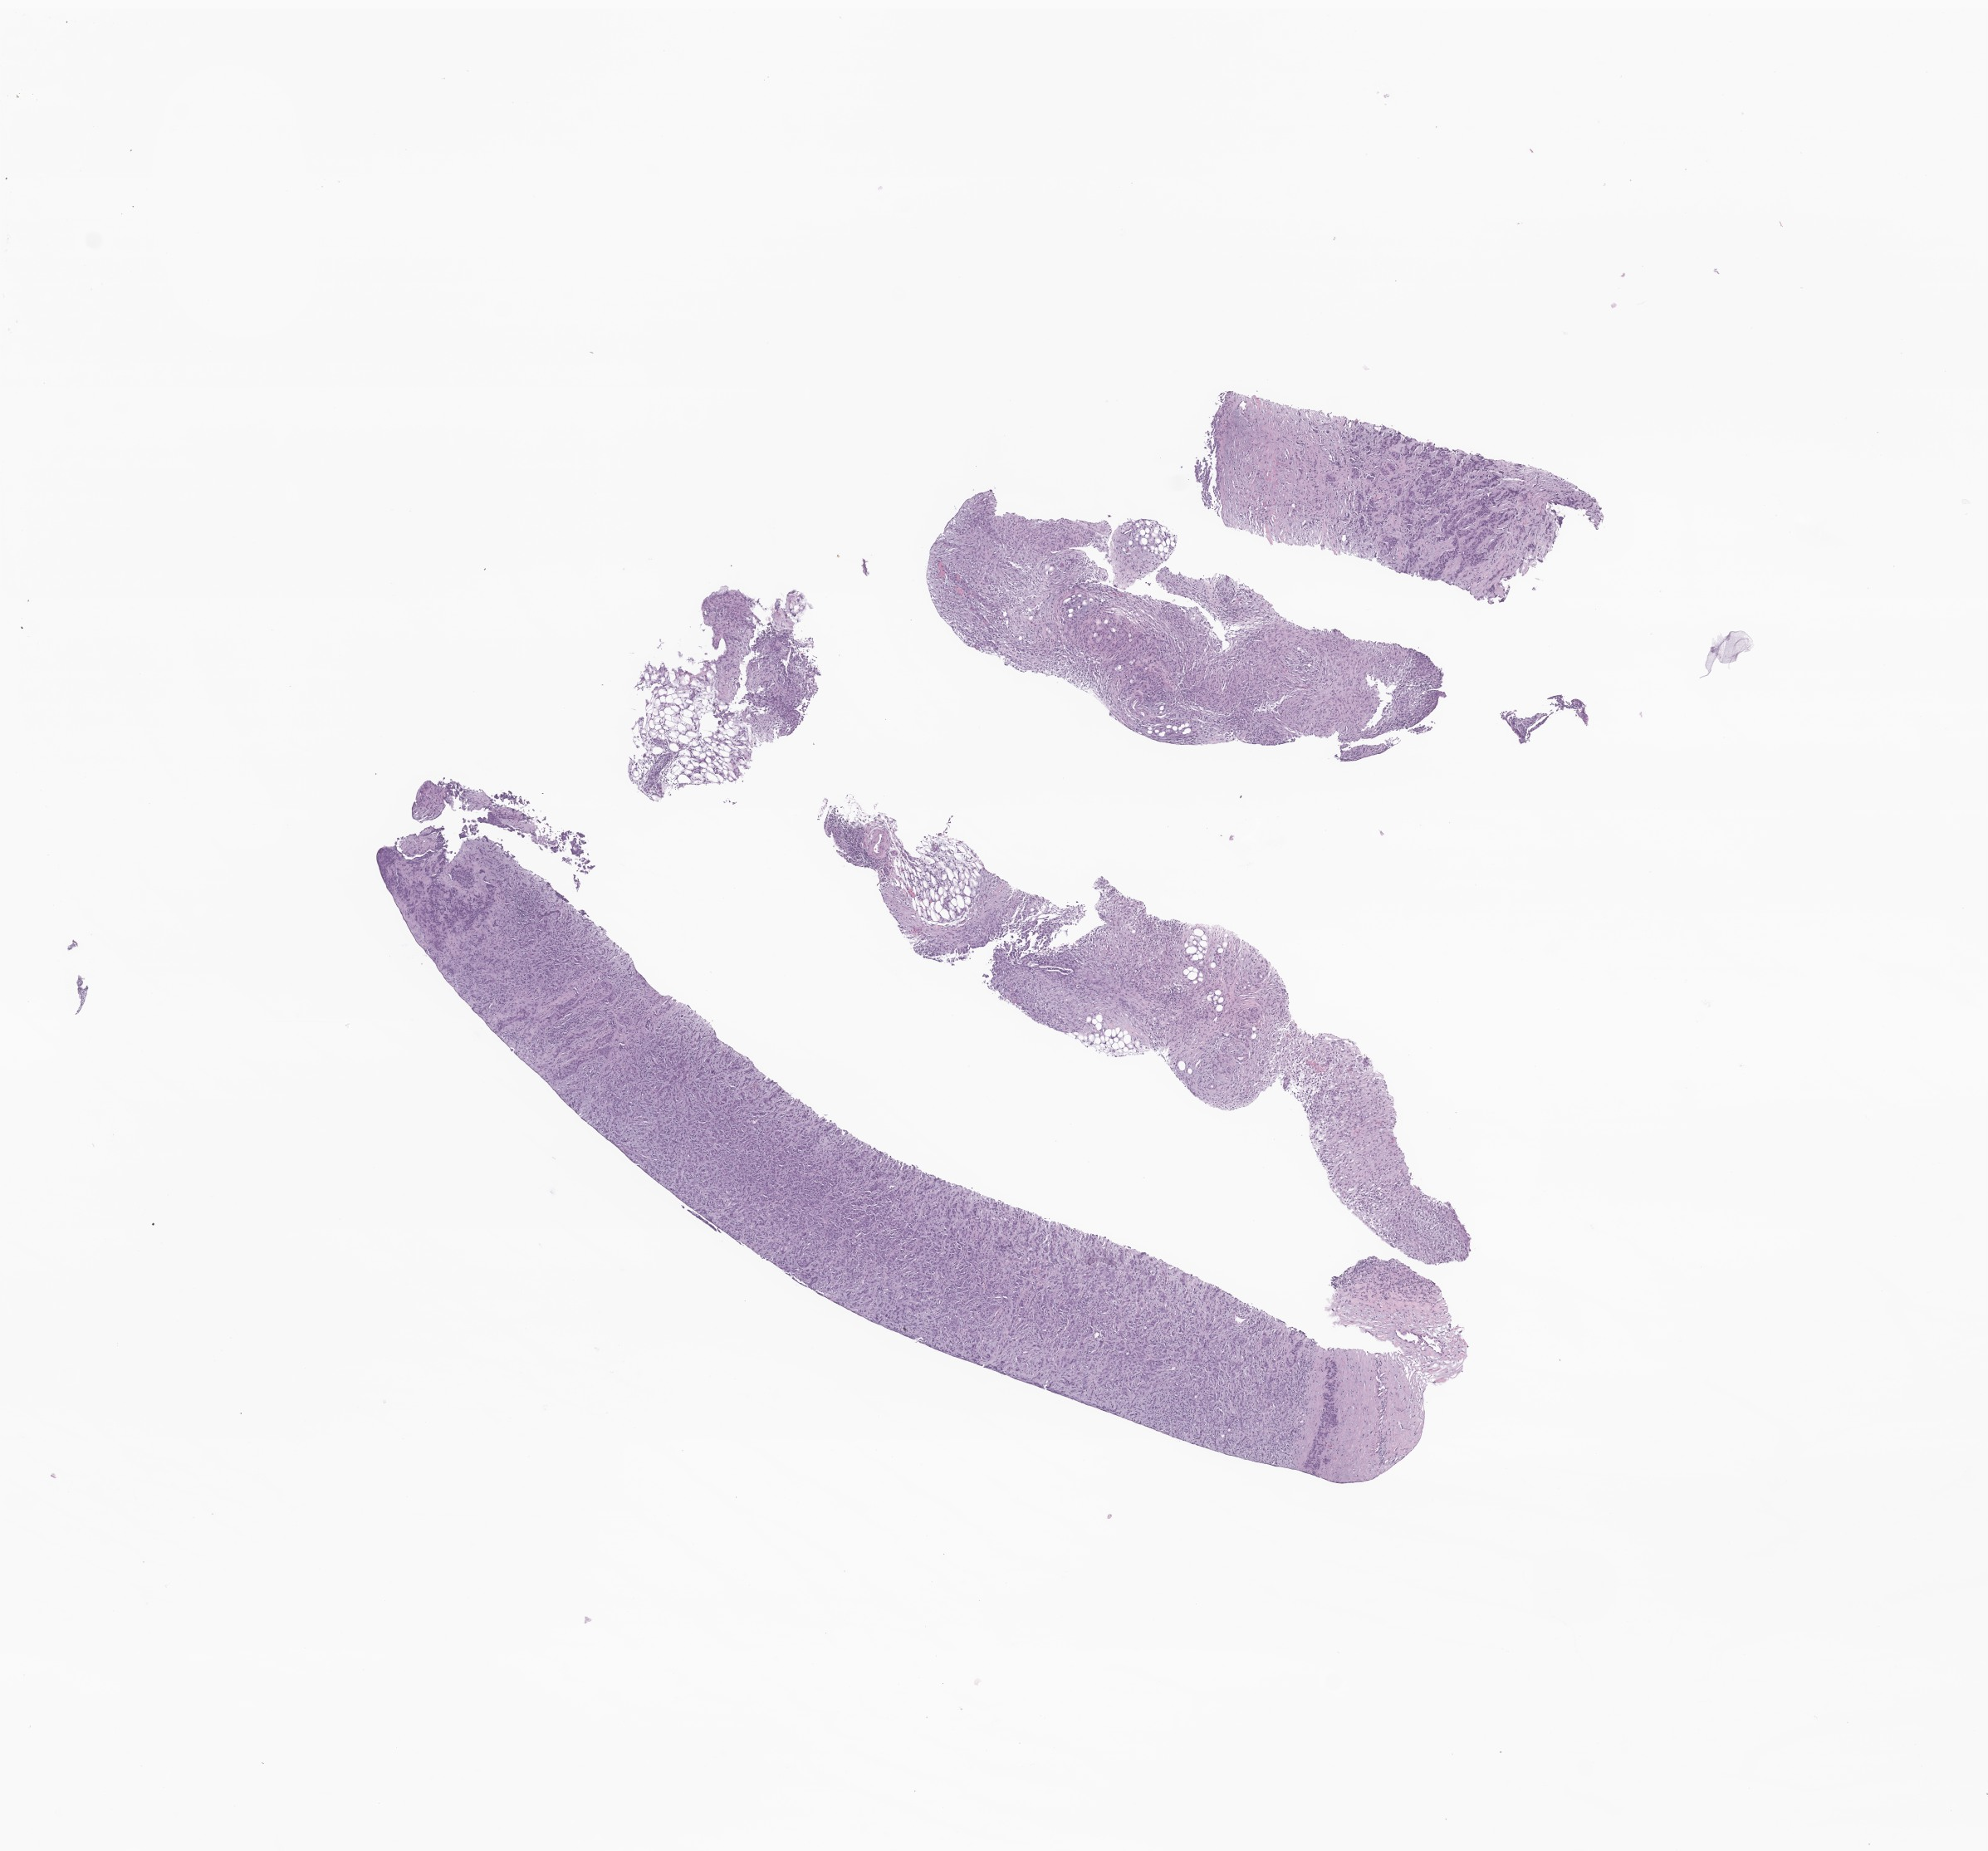
Digitized hematoxylin and eosin (H&E)-stained section of tumor tissue from the abdomen — a low-resolution overview of the entire scanned area, about 10.1 x 9.4 mm; formalin-fixed, paraffin-embedded (FFPE) tissue. Patient male; age 195 months (16 years 3 months).
Diagnosis (ICD-O-3 morphology term): Carcinomatosis.